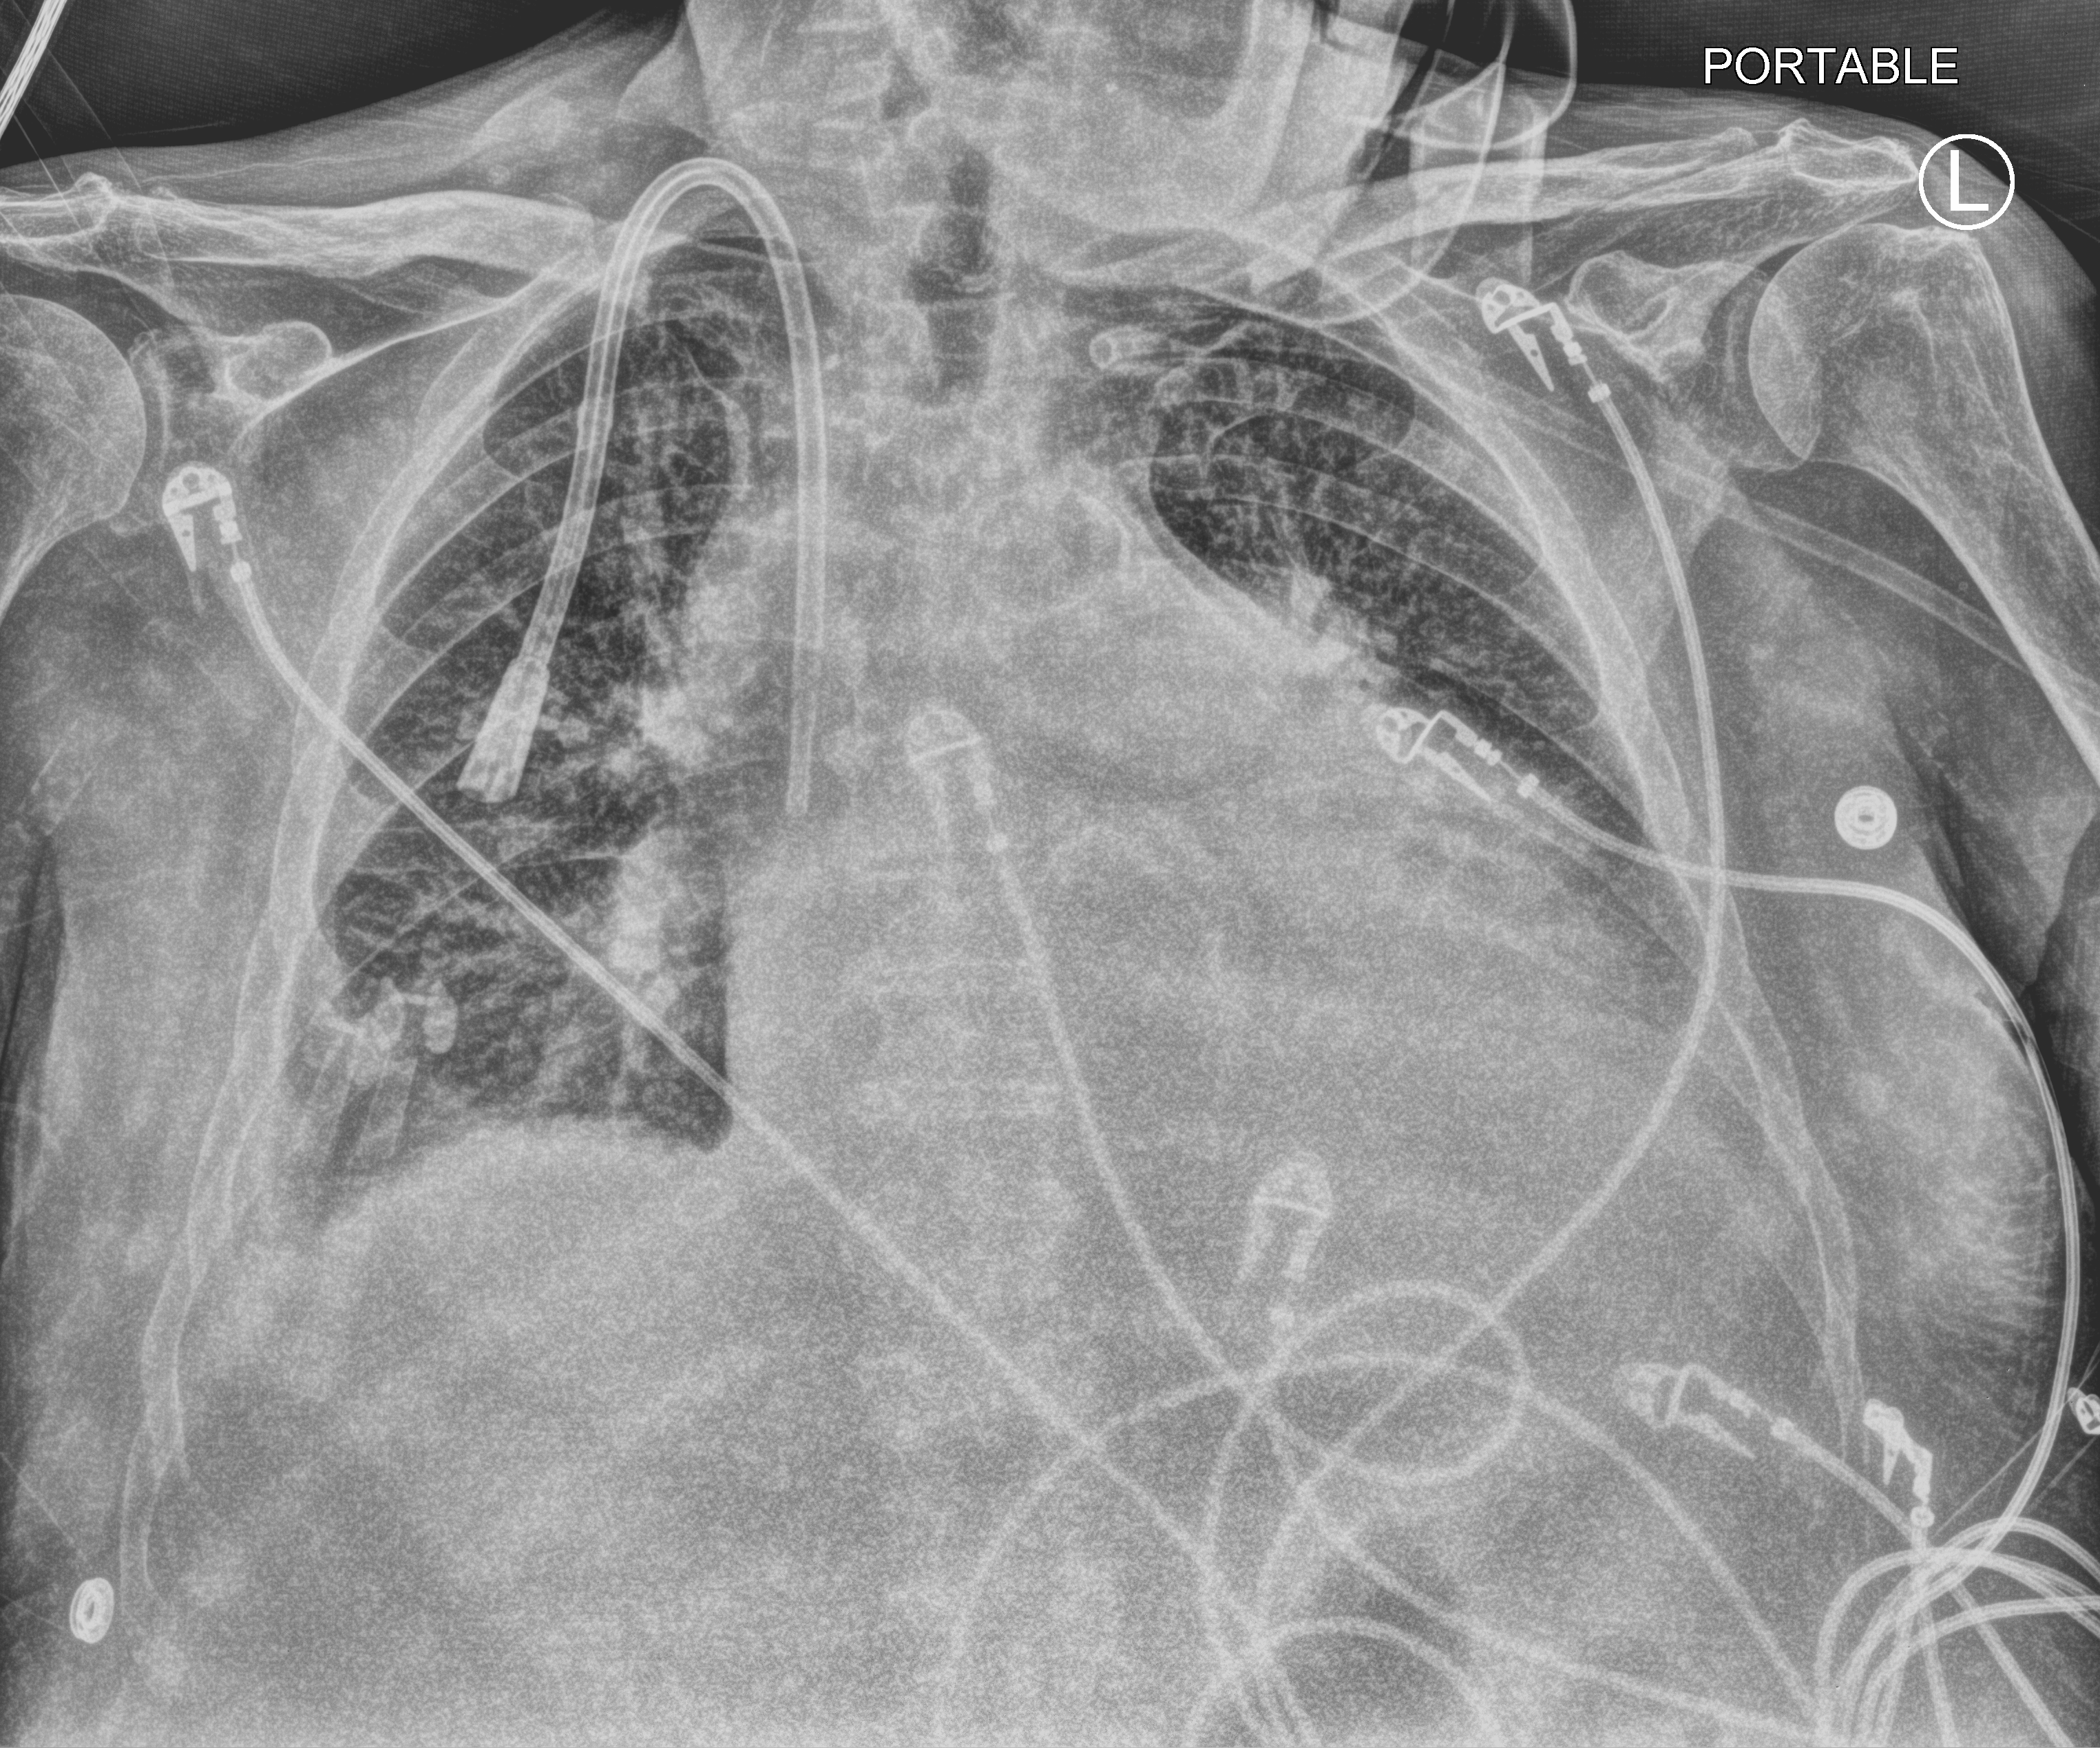
Chest X-ray (portable), anteroposterior (AP) projection. Male patient hospitalised with COVID-19, age 60–74 years.
Admission-level facts for this patient (not findings on this image; timing relative to this image not recorded): COPD (admission record): yes.